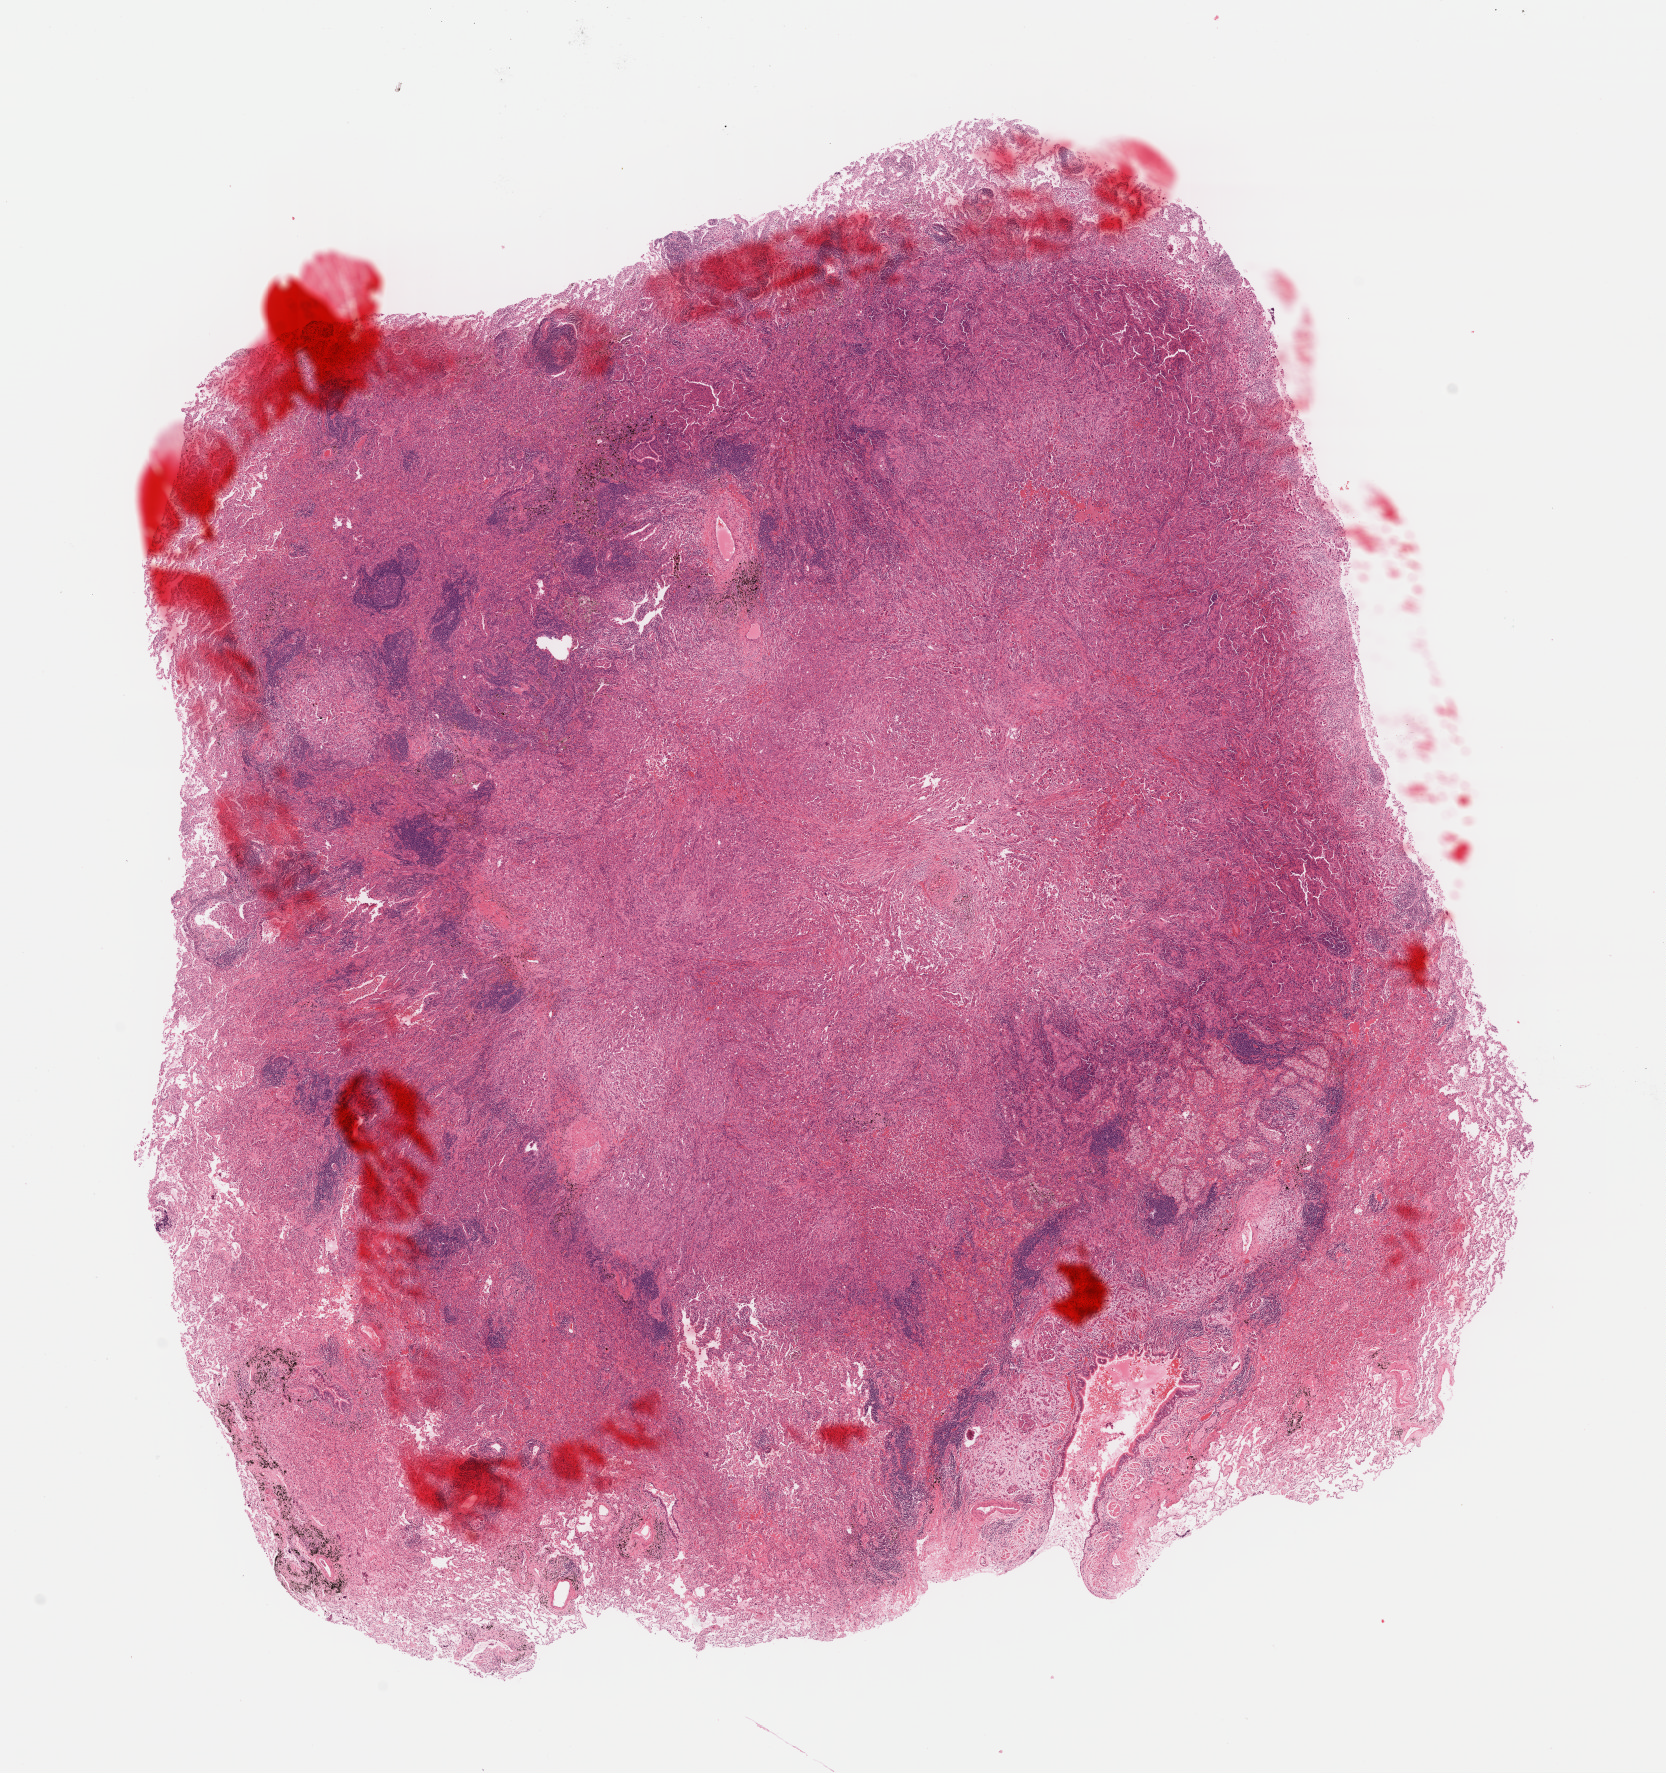
Whole-slide histology image, H&E-stained, shown as a low-resolution overview of the whole scanned area (about 13.1 x 13.9 mm), formalin-fixed paraffin-embedded (FFPE) diagnostic section, primary tumour sample from the lung. Patient: female, age at initial diagnosis 60 years.
- pathologic diagnosis: Squamous cell carcinoma, NOS (upper lobe, lung)
- AJCC pathologic stage: IA (7th edition)